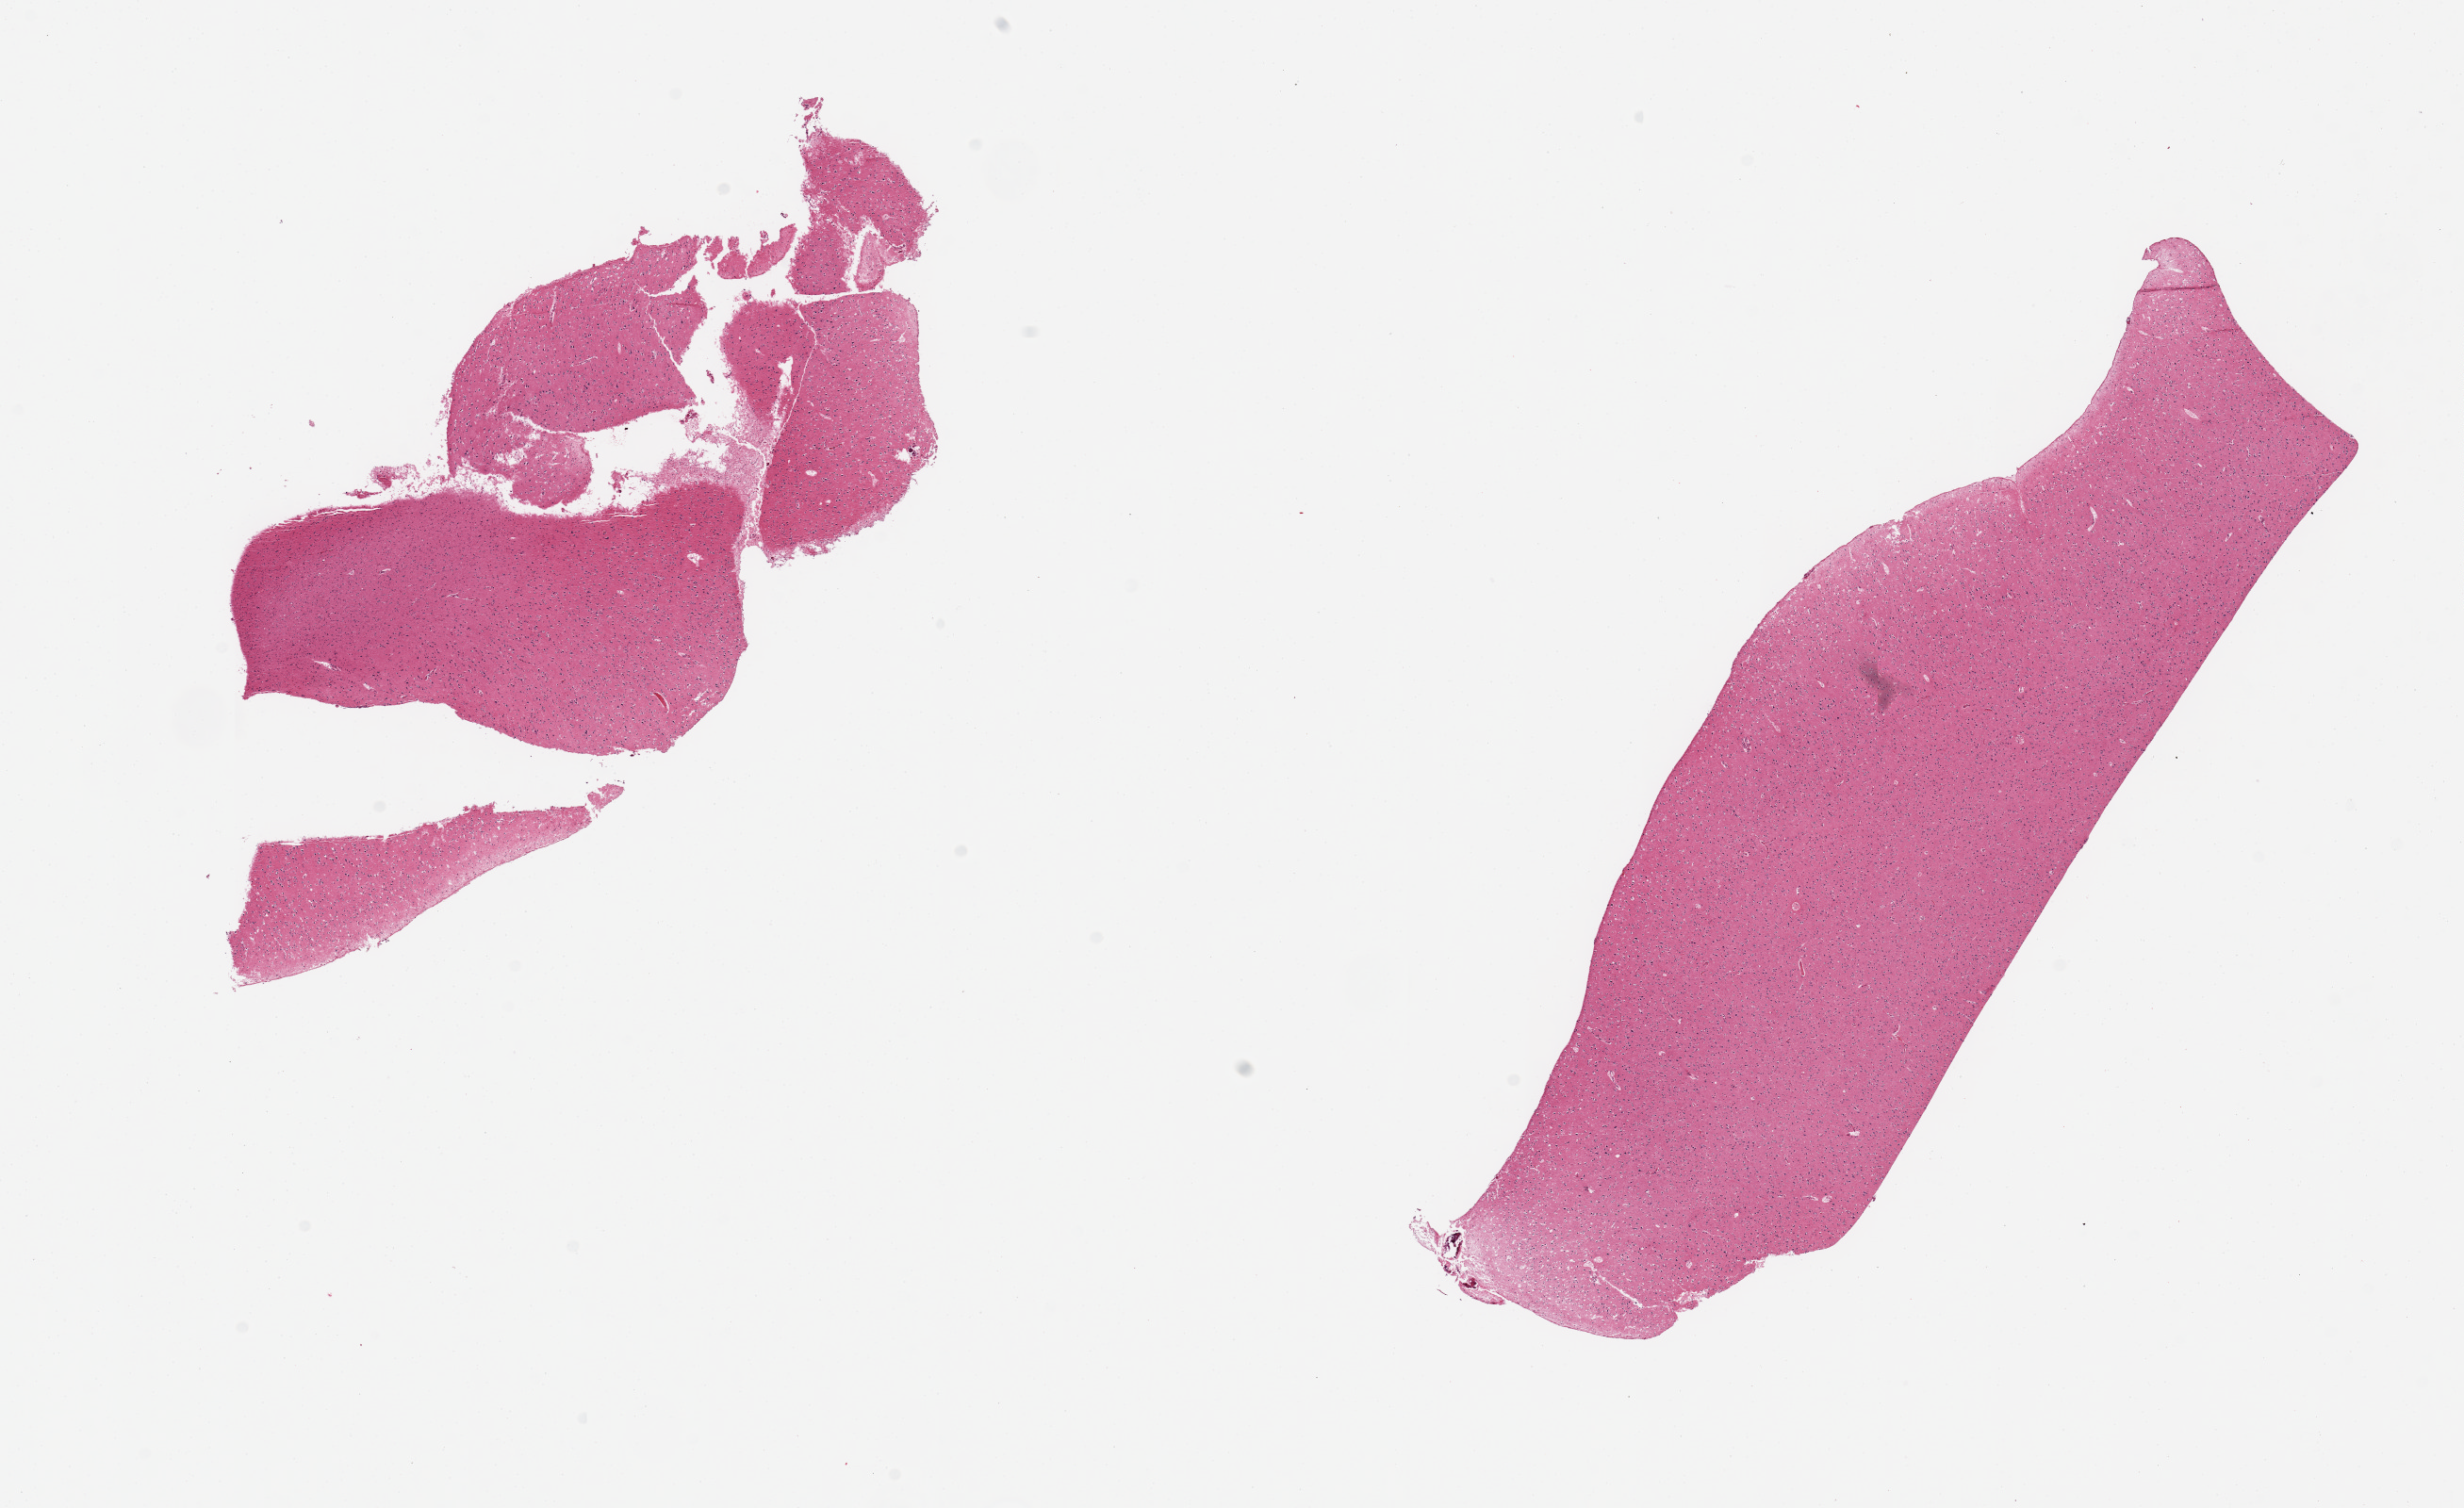
Whole-slide image, haematoxylin and eosin stain, brightfield, shown as a low-resolution overview of the whole scanned area (about 20.7 x 12.7 mm); PAXgene-fixed paraffin-embedded (PFPE) section; section of cerebral cortex (target tissue); tissue donor sample. Donor sex: male.
Review note (as recorded): 2 partly fragmented pieces.